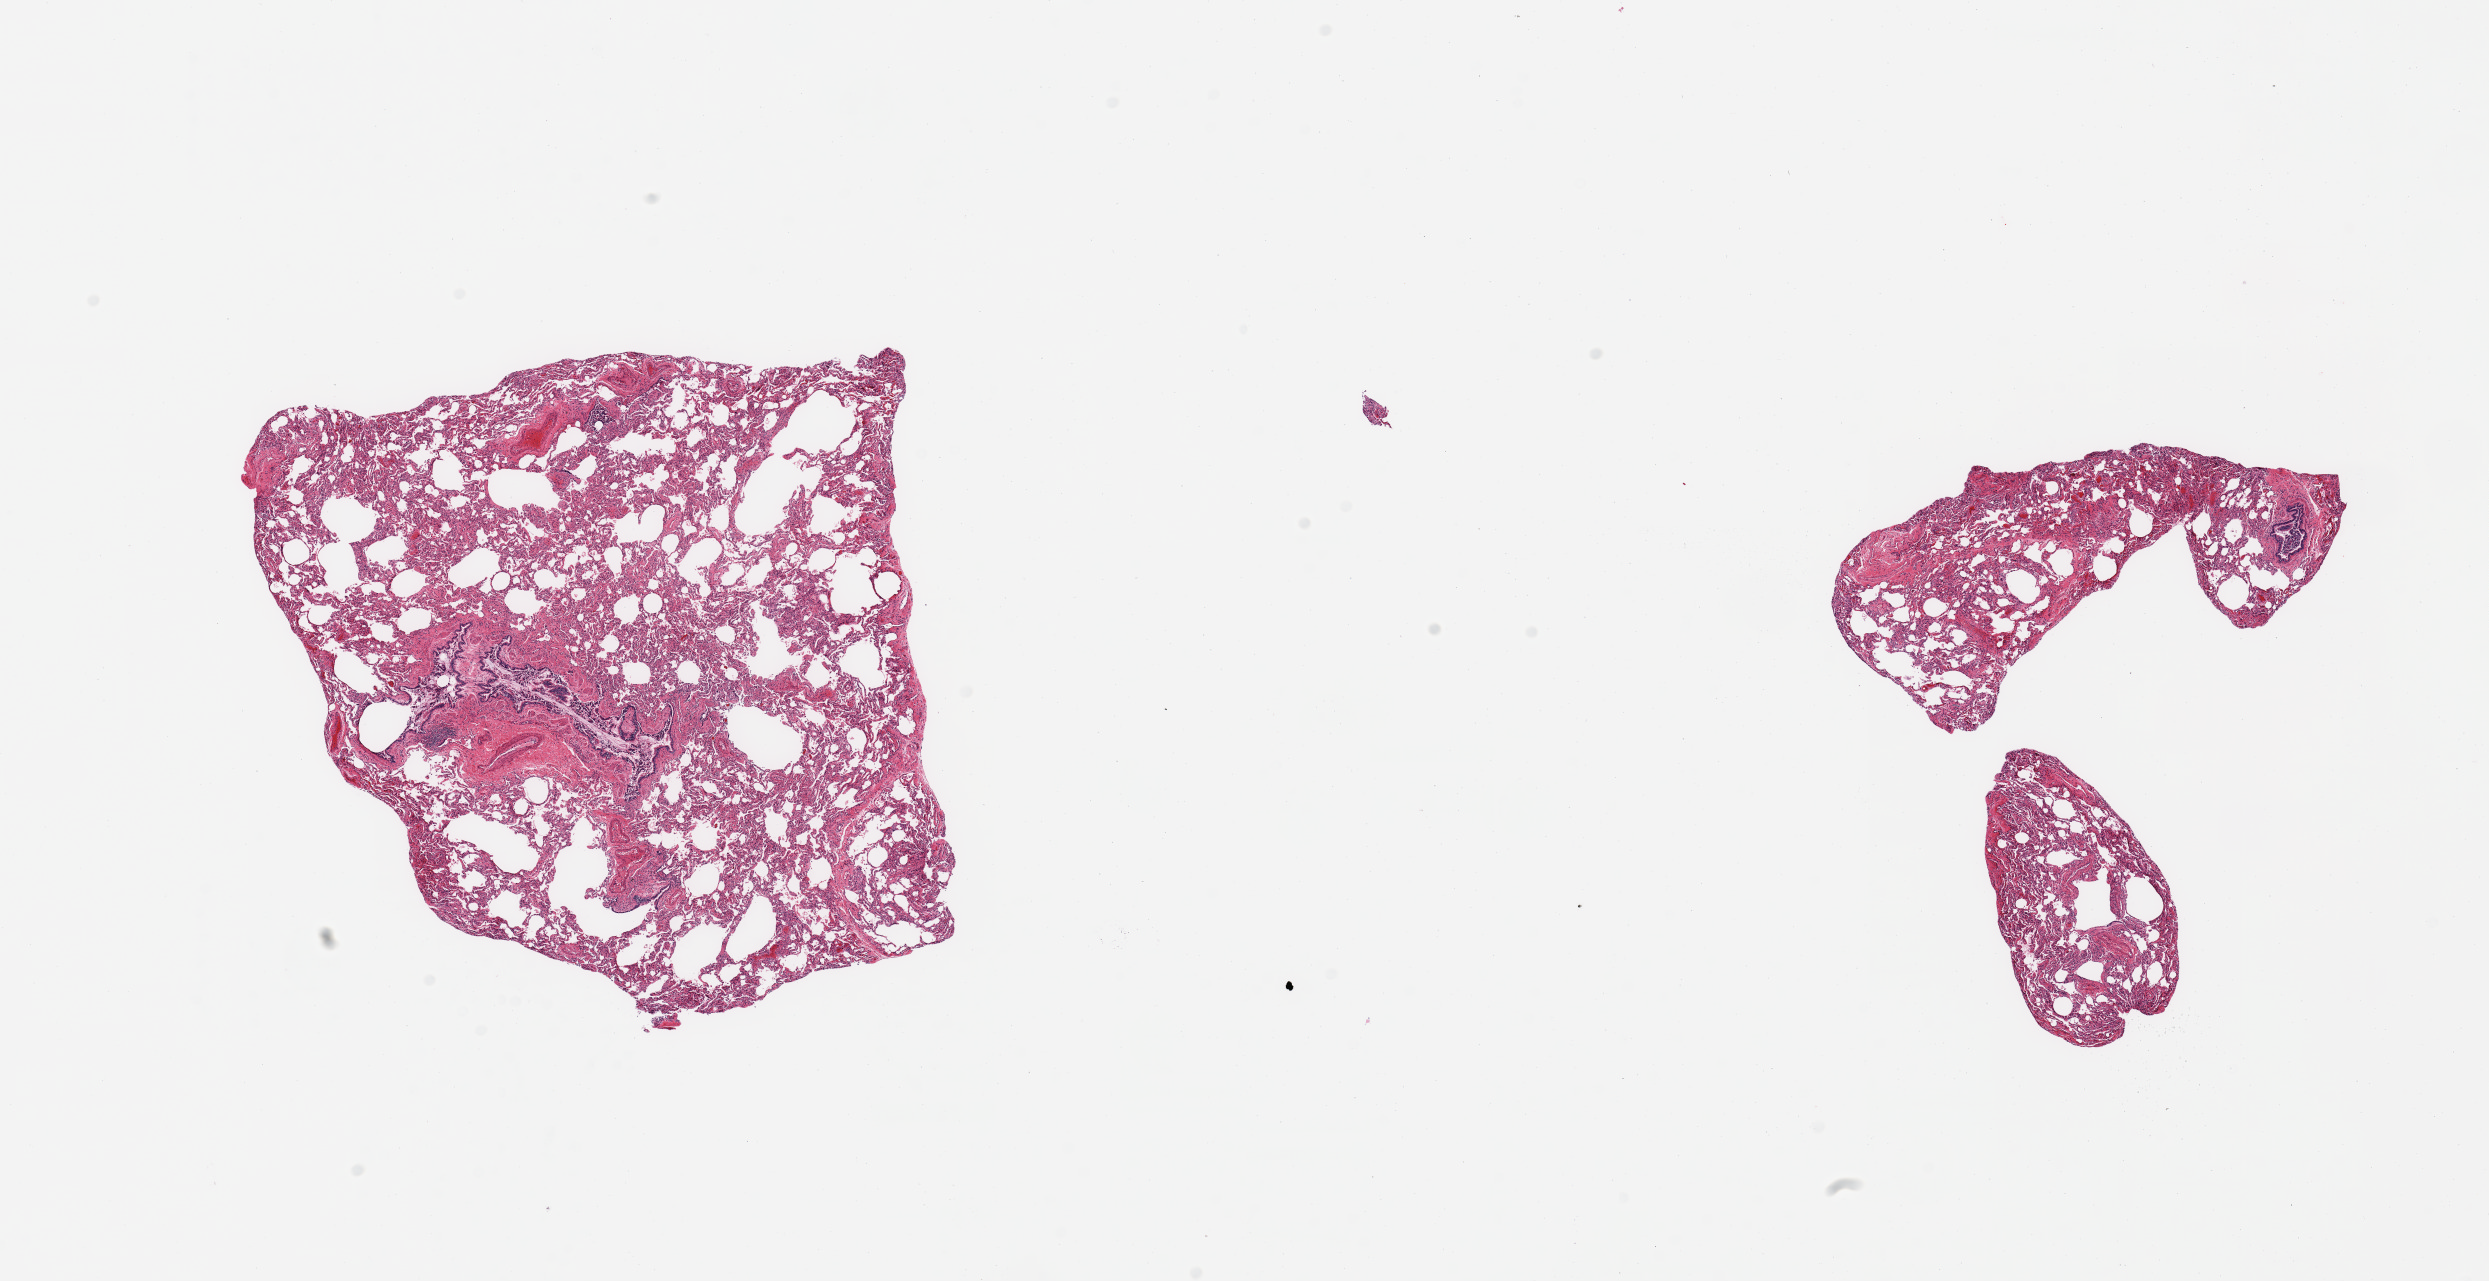
Whole-slide image, haematoxylin and eosin stain — shown as a low-resolution overview of the whole scanned area (about 19.7 x 10.1 mm), PAXgene-fixed, paraffin-embedded tissue, target tissue: lung, tissue donor sample. Donor: female.
Reviewer comment on this tissue sample: 2 pieces; no exudates or fibrosis; bronchus in larger piece.